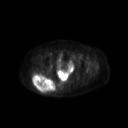
FDG PET of an extremity soft-tissue mass (from a PET/CT study), one axial slice. Position 55 of 267 along the scan axis. 3.27 mm slice thickness. 128 × 128 image matrix, field of view 600 × 600 mm. Patient: female, 60 years. From the clinical record (not read from this slice): histological type: spindle cell suggestive of myxofibrosarcoma; grade: intermediate; site of the primary tumour: right buttock.
Outlined on this slice (expert contour drawn on MRI and transferred to this co-registered scan by the dataset authors):
- gross tumour volume (mass): bounding box (x1, y1, x2, y2) in pixels: (33, 73, 56, 94)